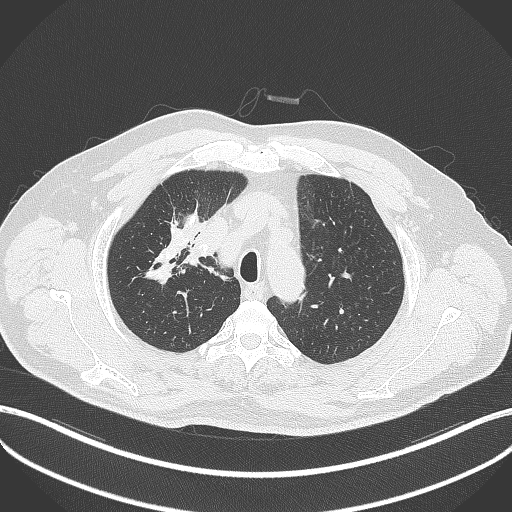
Chest CT, one axial slice. Reconstruction kernel B70f. 120 kVp. Lung window (W 1500 / L -600 HU). 1 mm slice thickness. 512 × 512 image matrix. Patient: male, 60 years. From the clinical record (not read from this slice): clinical TNM (as recorded): T1b N1 M0.
Structures marked on this image (bounding box drawn by a radiologist):
- lung tumour (recorded histology: squamous cell carcinoma): bounding box <180,242,207,266> (left, top, right, bottom; pixels)